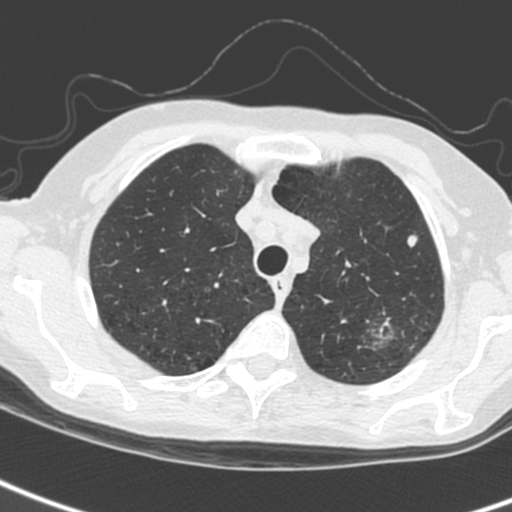
Low-dose screening chest CT, one axial slice; position 208 of 242 along the scan axis; 120 kVp; lung window (W 1500 / L -600 HU); 512 × 512 image matrix, field of view 284 × 284 mm.
Structures marked on this image (manually delineated by an expert):
- lesion 2 (tumor, upper lobe of left lung): box from (x=407, y=235) to (x=418, y=247) px